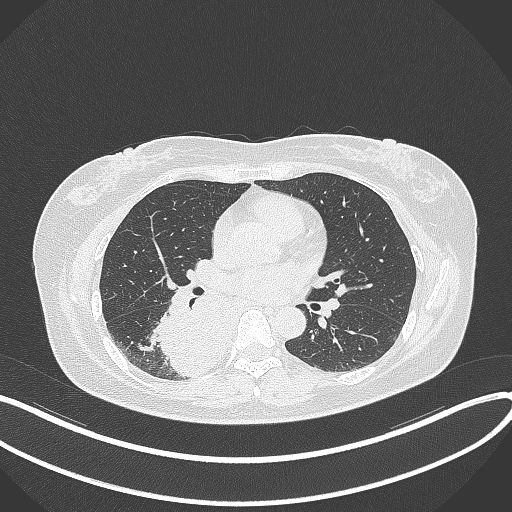
Chest CT, one axial slice; position 185 of 331 along the scan axis; reconstruction kernel B70f; 120 kVp; lung window (W 1500 / L -600 HU); 1 mm slice thickness; 512 × 512 image matrix. Female patient, age 54 years. Case-level facts recorded for this patient, not image findings: clinical TNM (as recorded): T4 N0 M0.
Outlined on this slice (bounding box drawn by a radiologist):
- lung tumour (recorded histology: adenocarcinoma): box from (x=148, y=275) to (x=245, y=385) px